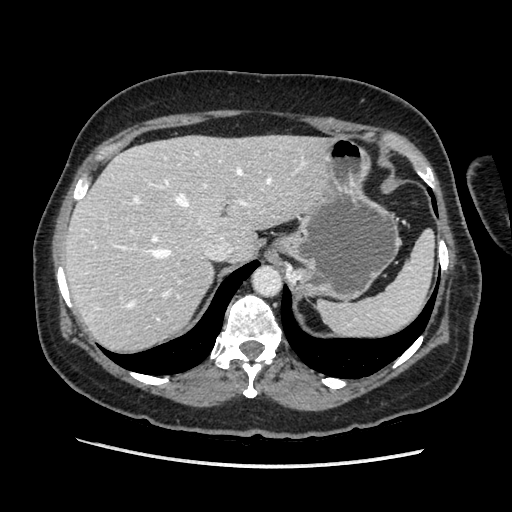
Contrast-enhanced abdominal CT, one axial slice. Position 149 of 203 along the scan axis. Soft-tissue window (W 400 / L 40 HU). 512 × 512 image matrix. Female patient. From the clinical record (not read from this slice): diagnosis: adrenocortical carcinoma; tumour side: left adrenal; tumour size at pathology: 6.5 cm; Ki-67 index: 22 %; stage (as recorded): 2.
Structures marked on this image (semi-automatic segmentation, software-assisted and operator-edited):
- mass: bounding box [x1, y1, x2, y2] px = [293, 269, 306, 280]